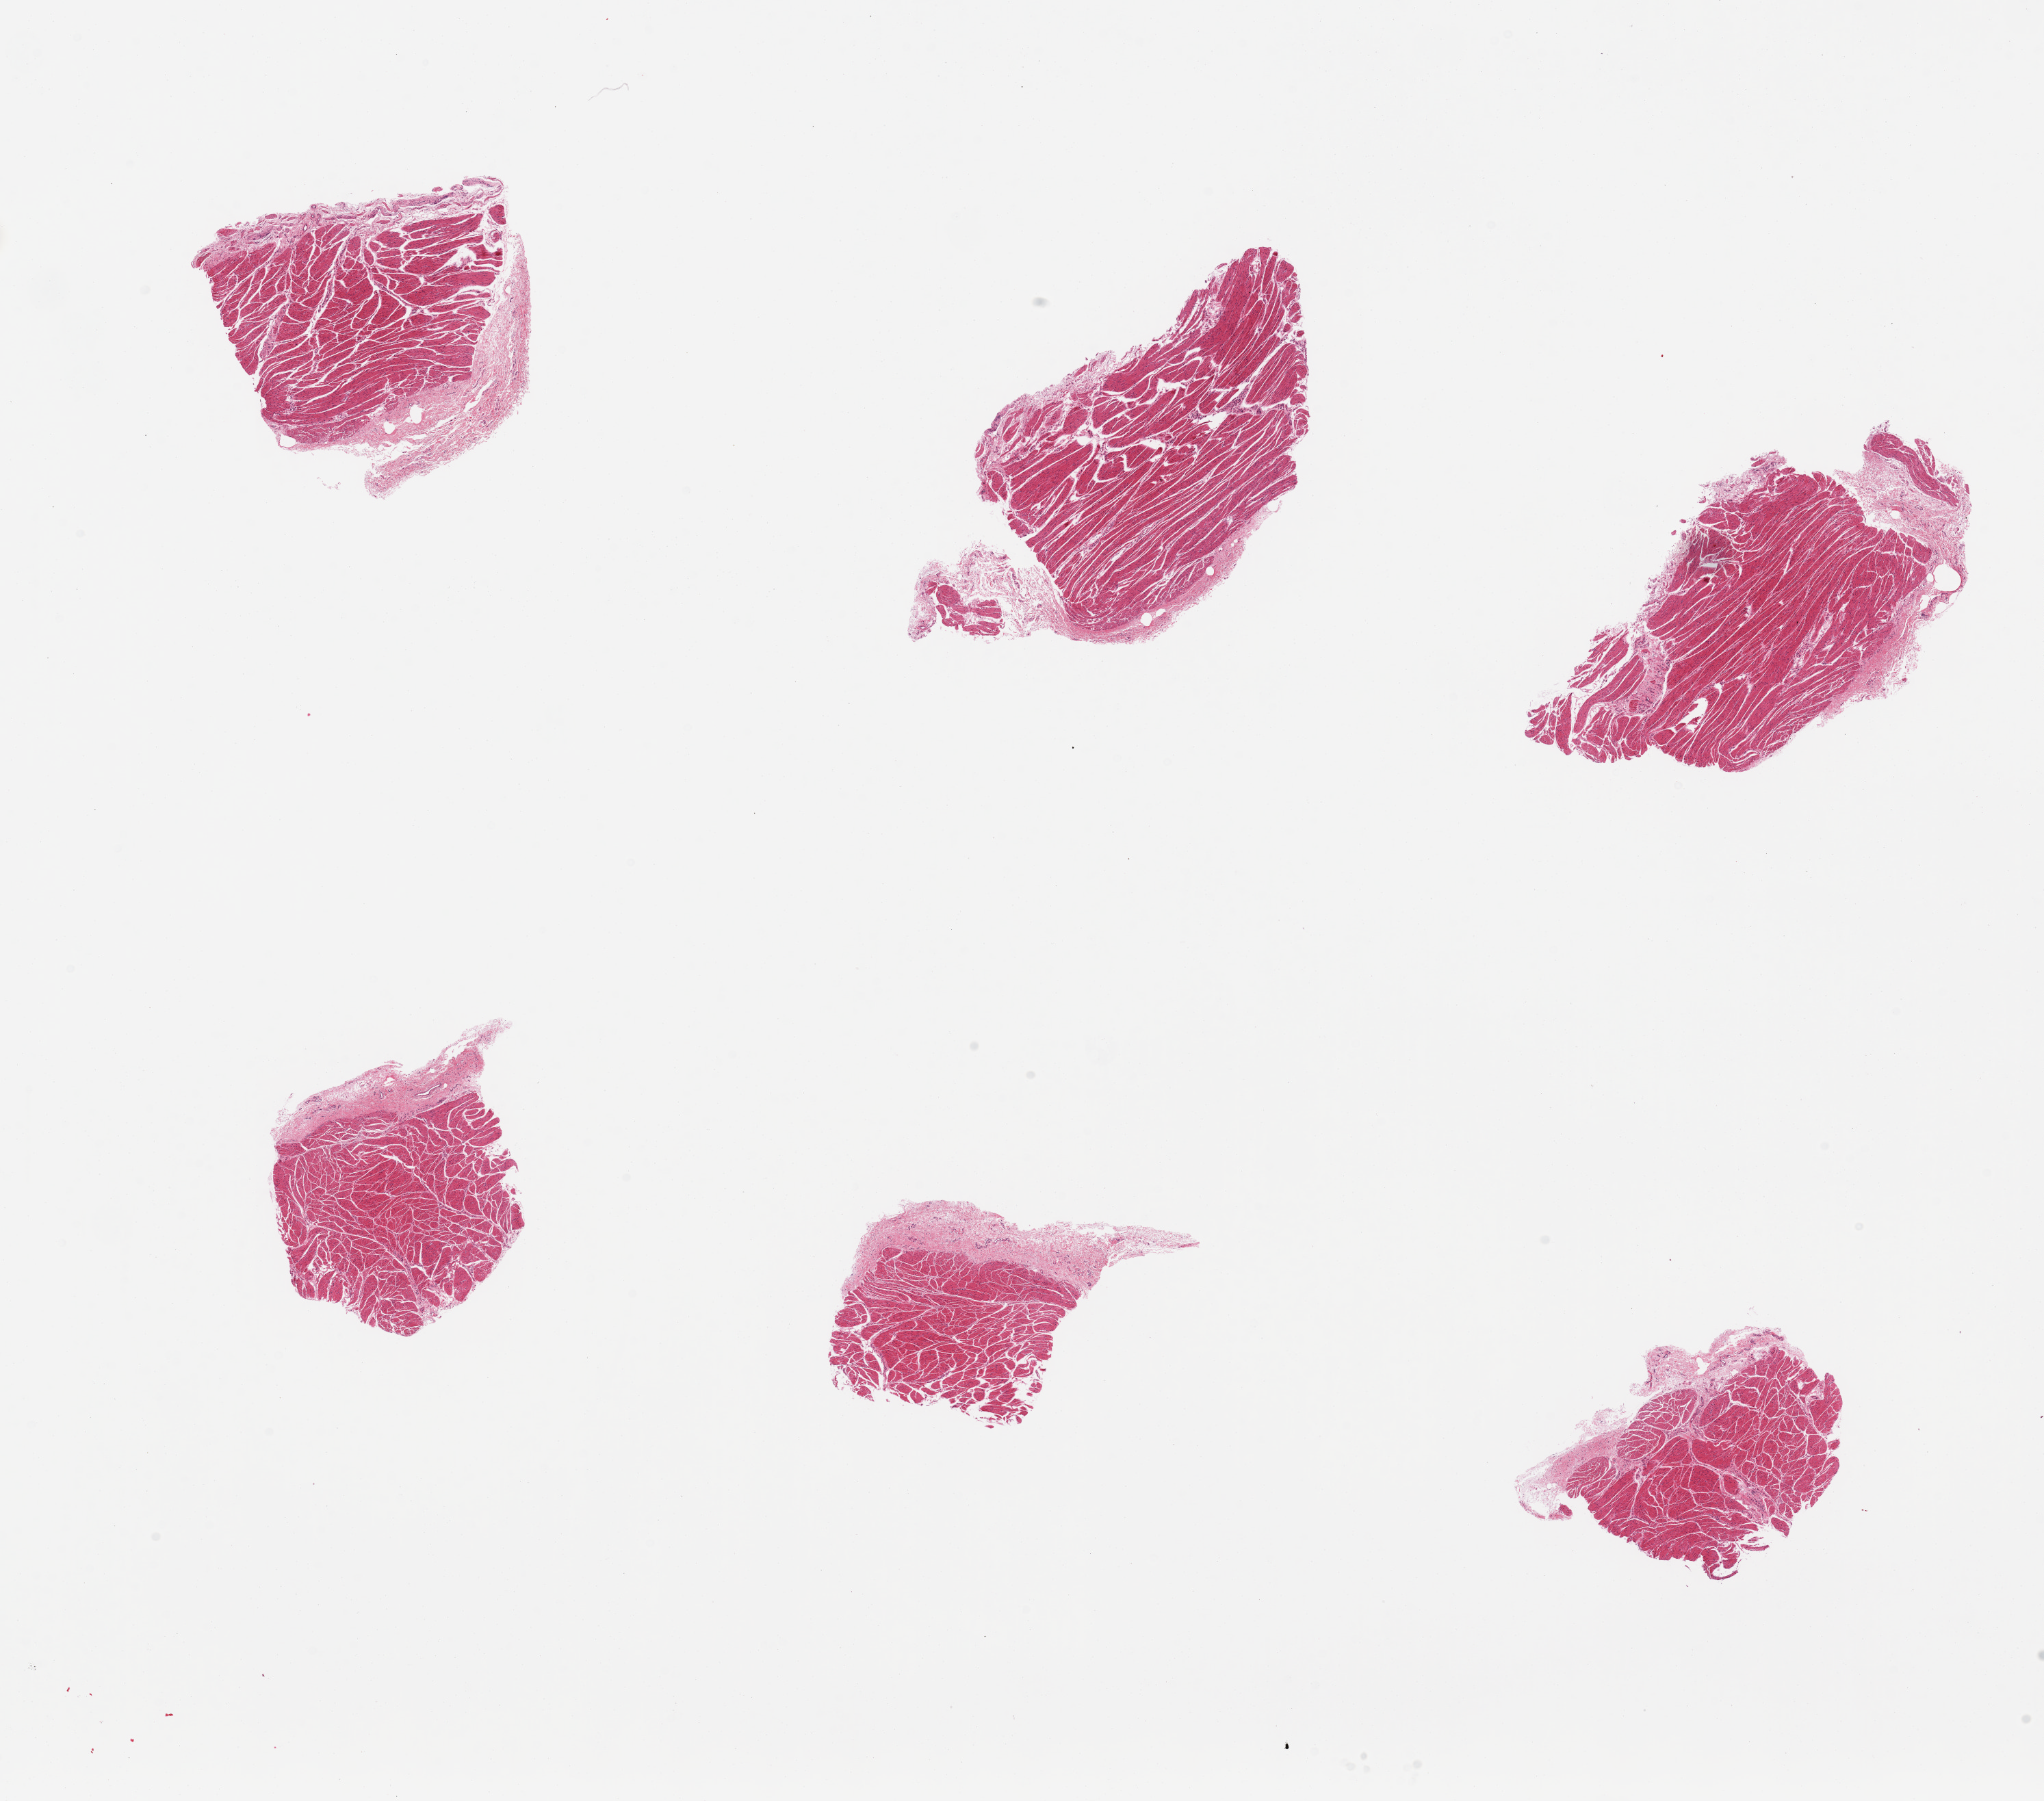
Hematoxylin and eosin (H&E) whole-slide image — low-resolution overview of the scanned area, about 23.6 x 20.8 mm (from a 20x scan). PAXgene-fixed paraffin-embedded (PFPE) section. Sampled site (target tissue): esophageal muscle. Tissue donor sample. Donor: male.
Review note (as recorded): 6 small pieces of muscularis.